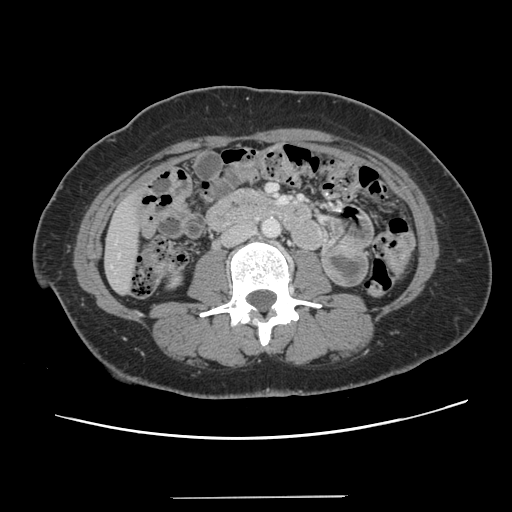
Contrast-enhanced abdominal CT, one axial slice. Position 27 of 141 along the scan axis. Soft-tissue window (W 400 / L 40 HU). 2.5 mm slice thickness. 512 × 512 image matrix, field of view 366 × 366 mm. Female patient, age 53 years. From the clinical record (not read from this slice): diagnosis: colorectal cancer liver metastases, imaged before liver resection.
Structures marked on this image (expert manual segmentation):
- liver: bounding box <106,199,139,292> (left, top, right, bottom; pixels)
- planned liver remnant (the part of the liver to remain after resection): <106,205,139,292>